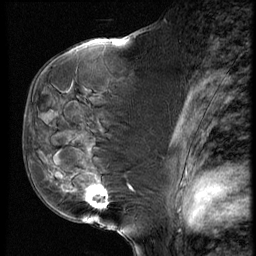
Breast MRI (dynamic contrast-enhanced), one sagittal slice; slice 33 of 60 in the series (ordered by position); dynamic contrast-enhanced series, image 2 of 4 at this slice position (ordered by acquisition); 1.5 T; TE 4.2 ms, TR 9 ms; 256 × 256 image matrix, field of view 180 × 180 mm. Patient: female, 50 years. Case-level facts recorded for this patient, not image findings: setting: breast cancer imaged before/during neoadjuvant chemotherapy; receptor status: HR-positive, HER2-negative.
Annotated regions visible in this slice (semi-automatic segmentation, software-assisted and operator-edited):
- analysis volume of interest (the breast-tissue region the enhancement analysis was run in; not a lesion): bounding box (x1, y1, x2, y2) in pixels: (48, 109, 135, 230)
- tumour enhancement mask (voxels above the 140 % enhancement threshold inside the analysis volume of interest): (85, 188, 108, 209)